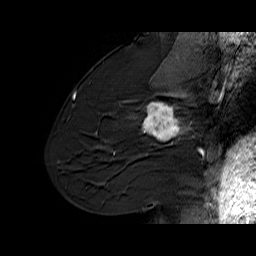
Breast MRI (dynamic contrast-enhanced), one sagittal slice; slice 36 of 60 in the series (ordered by position); dynamic contrast-enhanced series, time point 2 of 6 at this slice position (early post-contrast); 1.5 T; TE 6.1 ms, TR 32.9 ms; 4 mm slice thickness; 256 × 256 image matrix, field of view 220 × 220 mm. Female patient. Case-level facts recorded for this patient, not image findings: setting: breast cancer imaged before/during neoadjuvant chemotherapy; receptor status: HER2-positive.
Structures marked on this image (semi-automatic segmentation, software-assisted and operator-edited):
- analysis volume of interest (the breast-tissue region the enhancement analysis was run in; not a lesion): bounding box (x1, y1, x2, y2) in pixels: (127, 95, 194, 165)
- tumour enhancement mask (voxels above the 100 % enhancement threshold inside the analysis volume of interest): (142, 95, 189, 145)